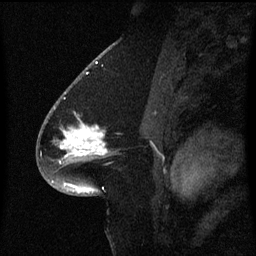
Breast MRI (dynamic contrast-enhanced), one sagittal slice; position 35 of 60 along the scan axis; dynamic contrast-enhanced series, image 2 of 3 at this slice position (ordered by acquisition); 1.5 T; TE 4.2 ms, TR 8.4 ms; 2 mm slice thickness; 256 × 256 image matrix. Female patient, age 54 years. From the clinical record (not read from this slice): setting: breast cancer imaged before/during neoadjuvant chemotherapy; receptor status: HR-positive, HER2-negative.
Annotated regions visible in this slice (semi-automatically segmented with operator editing):
- analysis volume of interest (the breast-tissue region the enhancement analysis was run in; not a lesion): box from (x=46, y=102) to (x=112, y=167) px
- tumour enhancement mask (voxels above the 70 % enhancement threshold inside the analysis volume of interest): (x=62, y=126)–(x=108, y=157)